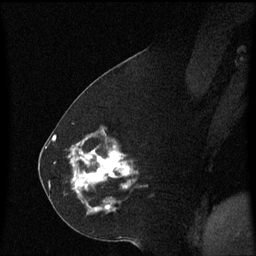
Breast MRI (dynamic contrast-enhanced), one sagittal slice; position 28 of 60 along the scan axis; dynamic contrast-enhanced series, image 2 of 3 at this slice position (ordered by acquisition); 1.5 T; TE 4.2 ms, TR 8.4 ms; 256 × 256 image matrix, field of view 200 × 200 mm. Patient: female, 60 years. From the clinical record (not read from this slice): setting: breast cancer imaged before/during neoadjuvant chemotherapy; receptor status: triple-negative.
Annotated regions visible in this slice (semi-automatic segmentation, software-assisted and operator-edited):
- analysis volume of interest (the breast-tissue region the enhancement analysis was run in; not a lesion): bounding box (x1, y1, x2, y2) in pixels: (69, 142, 136, 215)
- tumour enhancement mask (voxels above the 70 % enhancement threshold inside the analysis volume of interest): (73, 146, 135, 191)